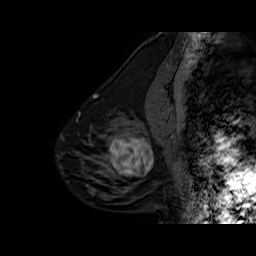
Breast MRI (dynamic contrast-enhanced), one sagittal slice. Slice 19 of 60 in the series (ordered by position). Dynamic contrast-enhanced series, time point 2 of 6 at this slice position (early post-contrast). 1.5 T. TE 6.3 ms, TR 32.5 ms. 256 × 256 image matrix. Female patient. From the clinical record (not read from this slice): setting: breast cancer imaged before/during neoadjuvant chemotherapy; receptor status: triple-negative.
Outlined on this slice (semi-automatically segmented with operator editing):
- analysis volume of interest (the breast-tissue region the enhancement analysis was run in; not a lesion): bounding box [x1, y1, x2, y2] px = [102, 127, 162, 186]
- tumour enhancement mask (voxels above the 100 % enhancement threshold inside the analysis volume of interest): [109, 137, 154, 176]